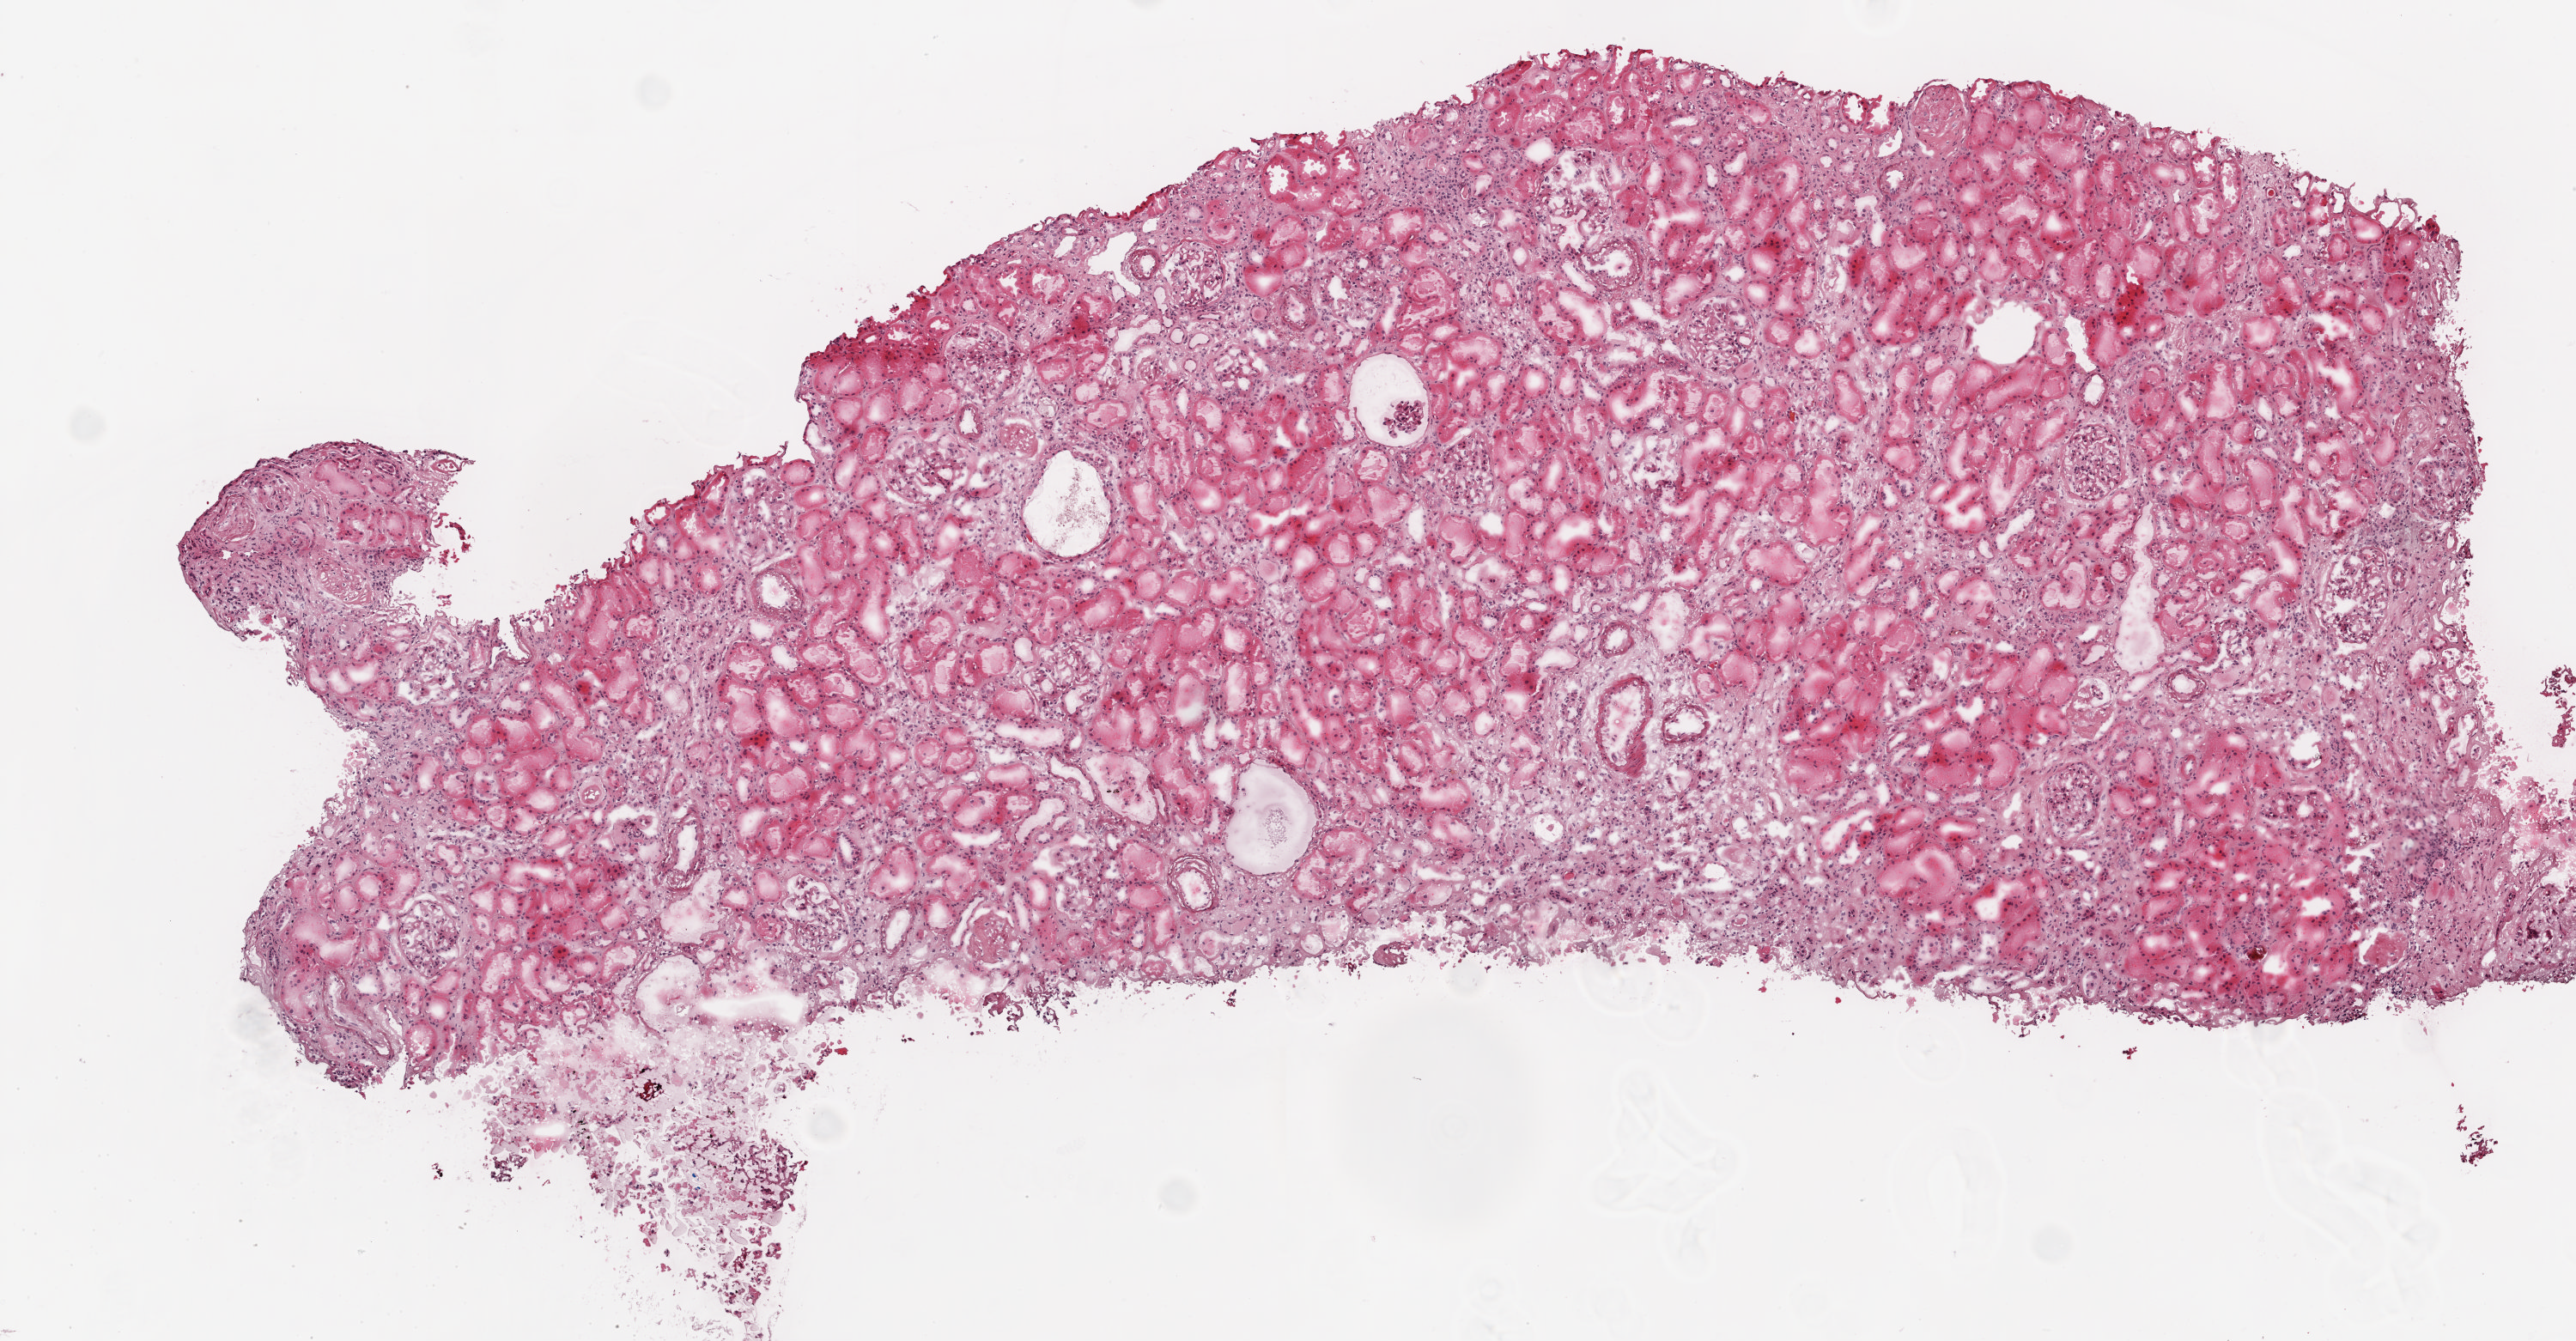
Whole-slide histology image, H&E-stained — whole scanned area (about 6.0 x 3.1 mm) shown as a low-resolution overview. Frozen section from the top of the tissue portion. Kidney, solid tissue normal (non-tumour tissue) sample. Patient: male, age at initial diagnosis 76 years.
This section: solid tissue normal (non-tumour) sample from the same patient. Patient diagnosis: Clear cell adenocarcinoma, NOS.